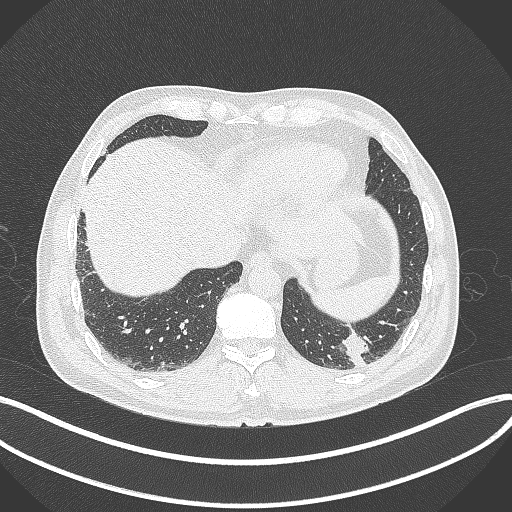
Chest CT, one axial slice. Lung window (W 1500 / L -600 HU). 1 mm slice thickness. 512 × 512 image matrix. Patient: male, 54 years. Case-level facts recorded for this patient, not image findings: clinical TNM (as recorded): T1c N0 M1; histopathological grade: G3.
Outlined on this slice (bounding box drawn by a radiologist):
- lung tumour (recorded histology: adenocarcinoma): box from (x=340, y=329) to (x=368, y=371) px